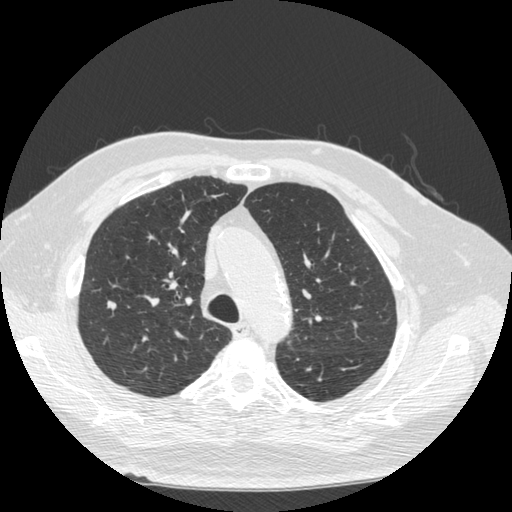
Low-dose screening chest CT, axial slice; second annual screen; lung window (W 1500 / L -600 HU); slice 155 of 221 in the series; 512 × 512 image matrix, field of view 360 × 360 mm. Male participant, aged 72 years at enrolment. Former smoker at enrolment.
• Expert reader's lesion annotation, bounding box [x1, y1, x2, y2] px = [88, 291, 124, 321].
• Screening reader's record for this exam: no non-calcified nodule ≥4 mm recorded.
• Official screen result: negative screen, minor abnormalities not suspicious for lung cancer.
• Lung cancer was diagnosed 449 days after this screen (after the third annual screen): squamous cell carcinoma, NOS, right upper lobe, poorly differentiated (G3), stage IIIA (AJCC 6th edition), 19 mm at pathology.